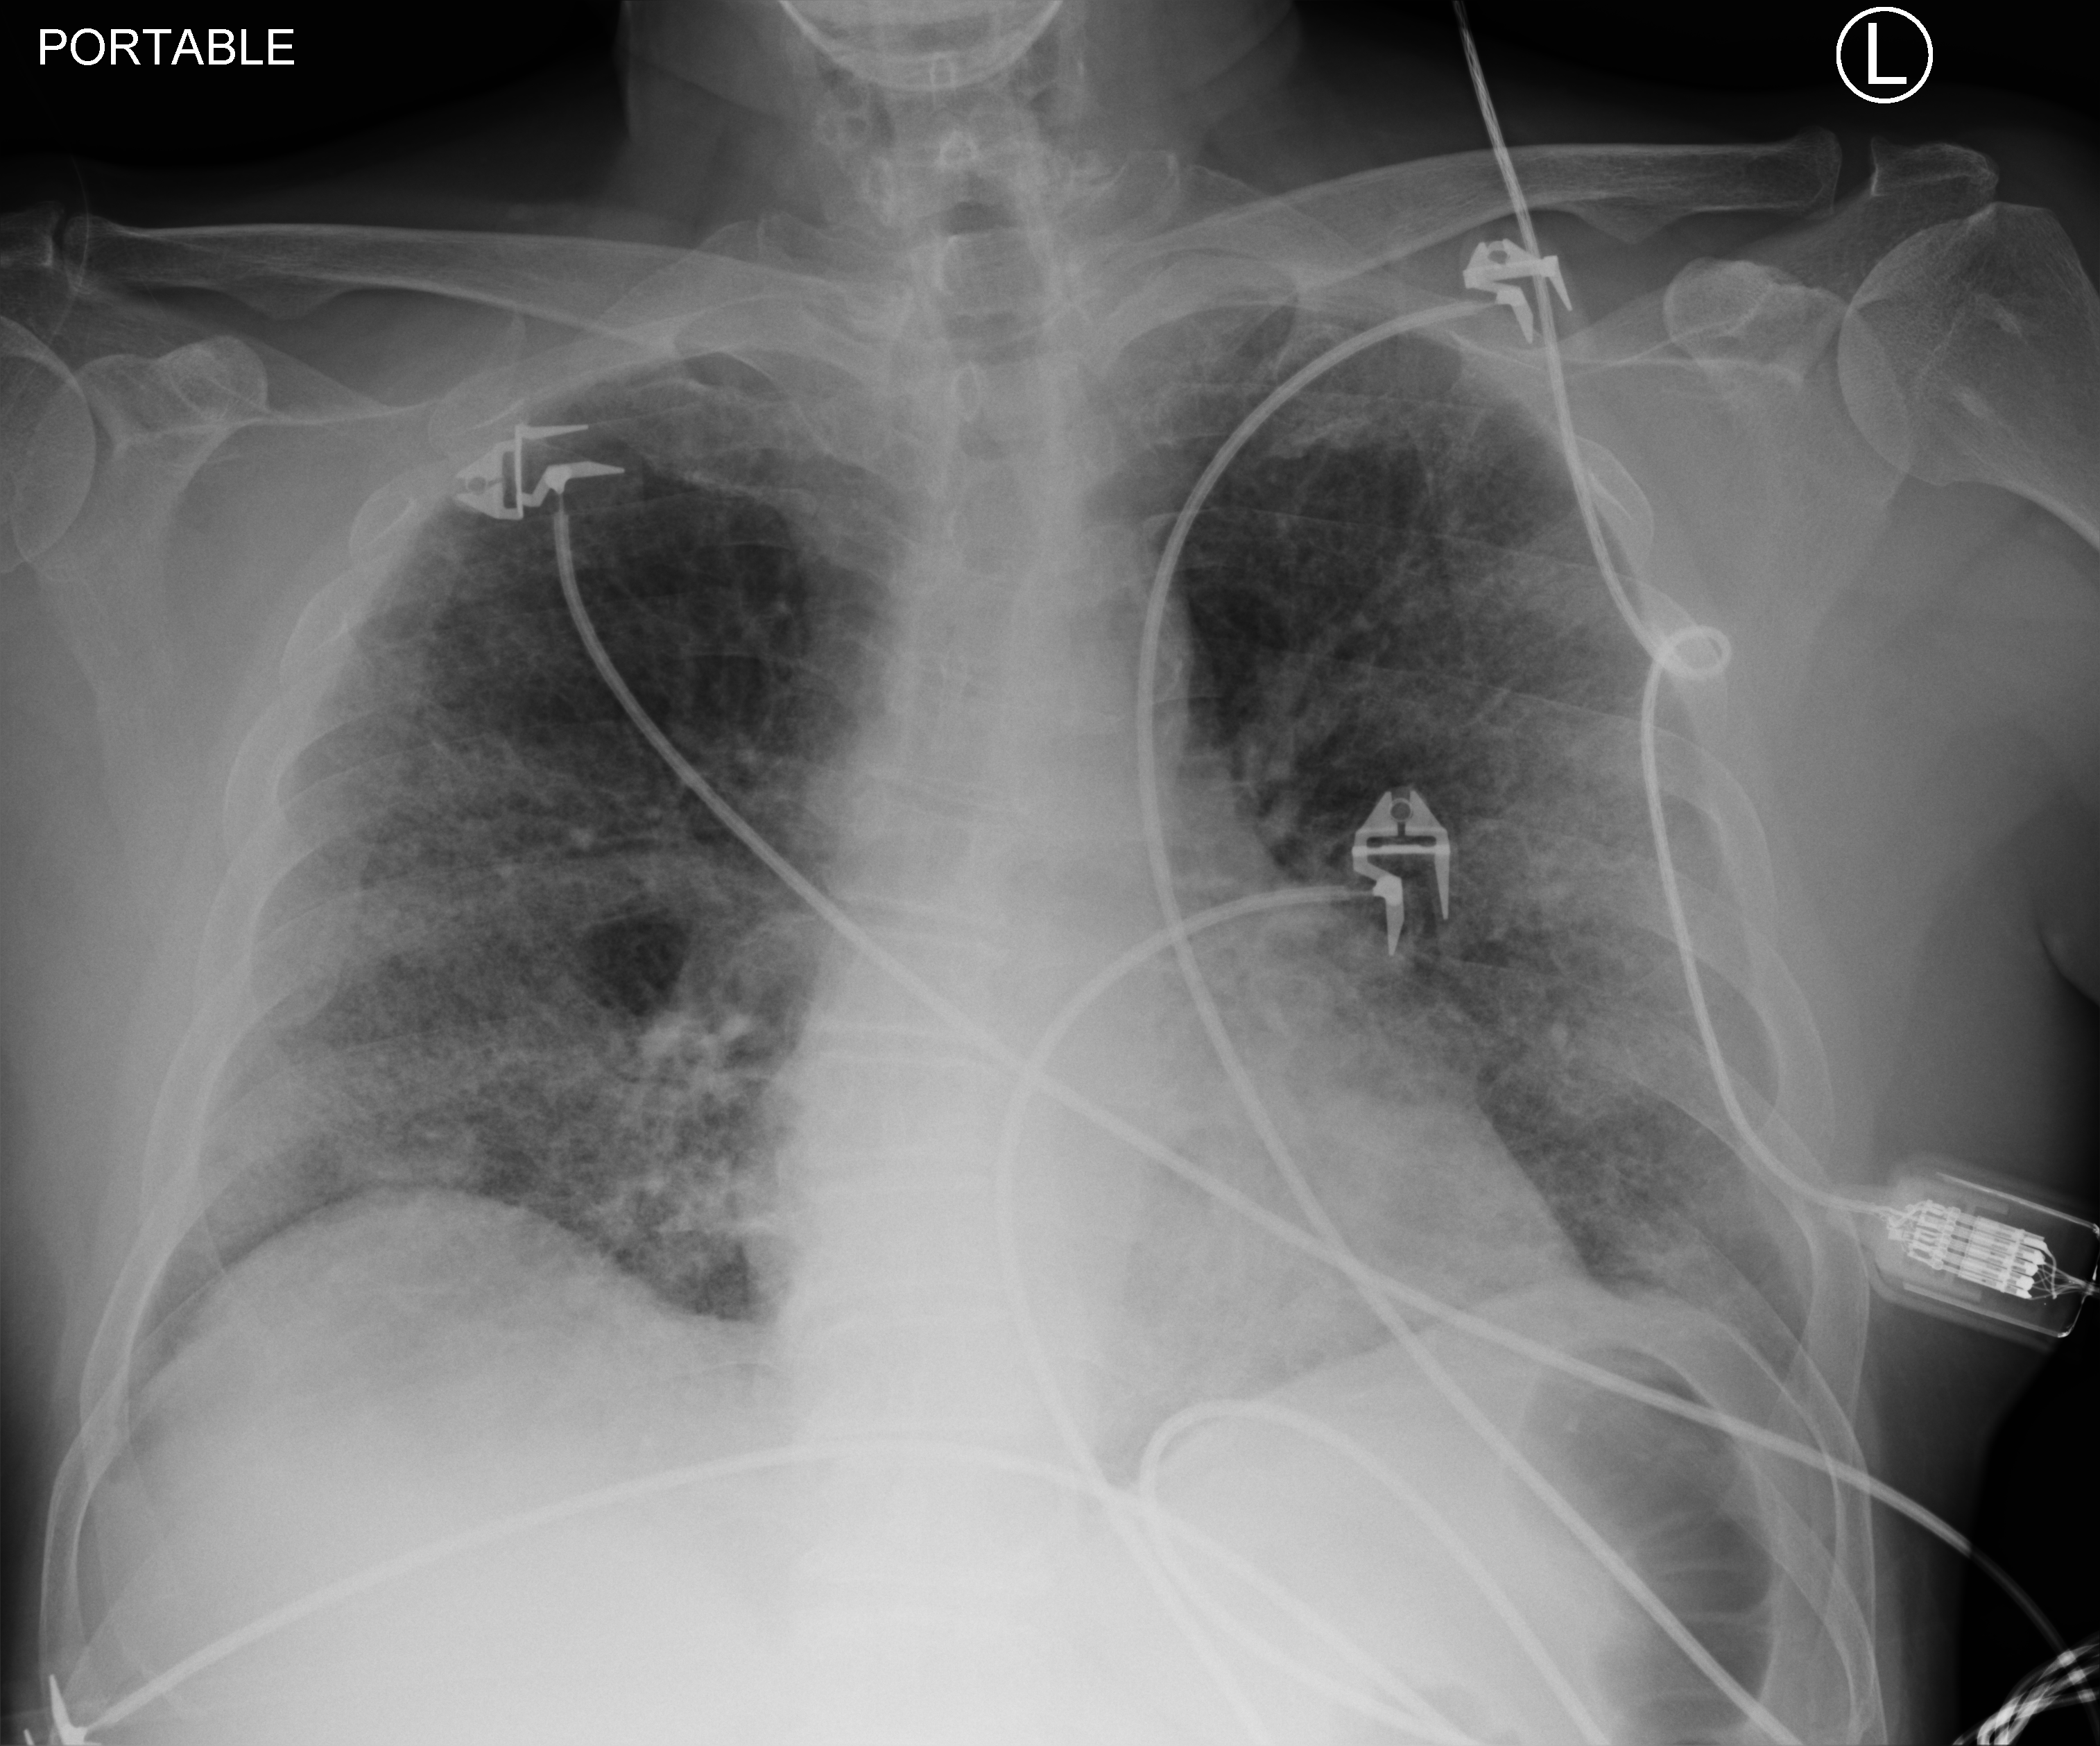
Chest X-ray (portable); anteroposterior (AP) projection. Male patient hospitalised with COVID-19, age 18–59 years.
Admission-level facts for this patient (not findings on this image; timing relative to this image not recorded): mechanically ventilated during this hospital stay: no.